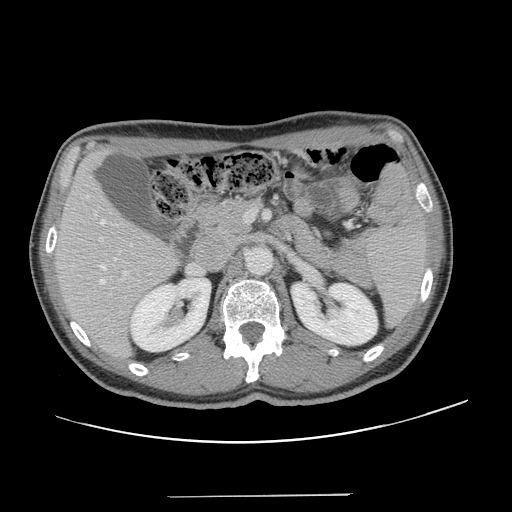
Contrast-enhanced abdominal CT, one axial slice. Slice 73 of 131 in the series (ordered by position). 120 kVp. Intravenous contrast given. Soft-tissue window (W 400 / L 40 HU). 2.5 mm slice thickness. 512 × 512 image matrix. Male patient, age 60 years. From the clinical record (not read from this slice): diagnosis: colorectal cancer liver metastases, imaged before liver resection; multiple liver metastases: no; largest metastasis: 2.5 cm; disease in both lobes: no.
Annotated regions visible in this slice (expert manual segmentation):
- hepatic veins: bounding box (x1, y1, x2, y2) in pixels: (100, 220, 117, 284)
- liver: (56, 153, 178, 359)
- planned liver remnant (the part of the liver to remain after resection): (56, 152, 178, 358)